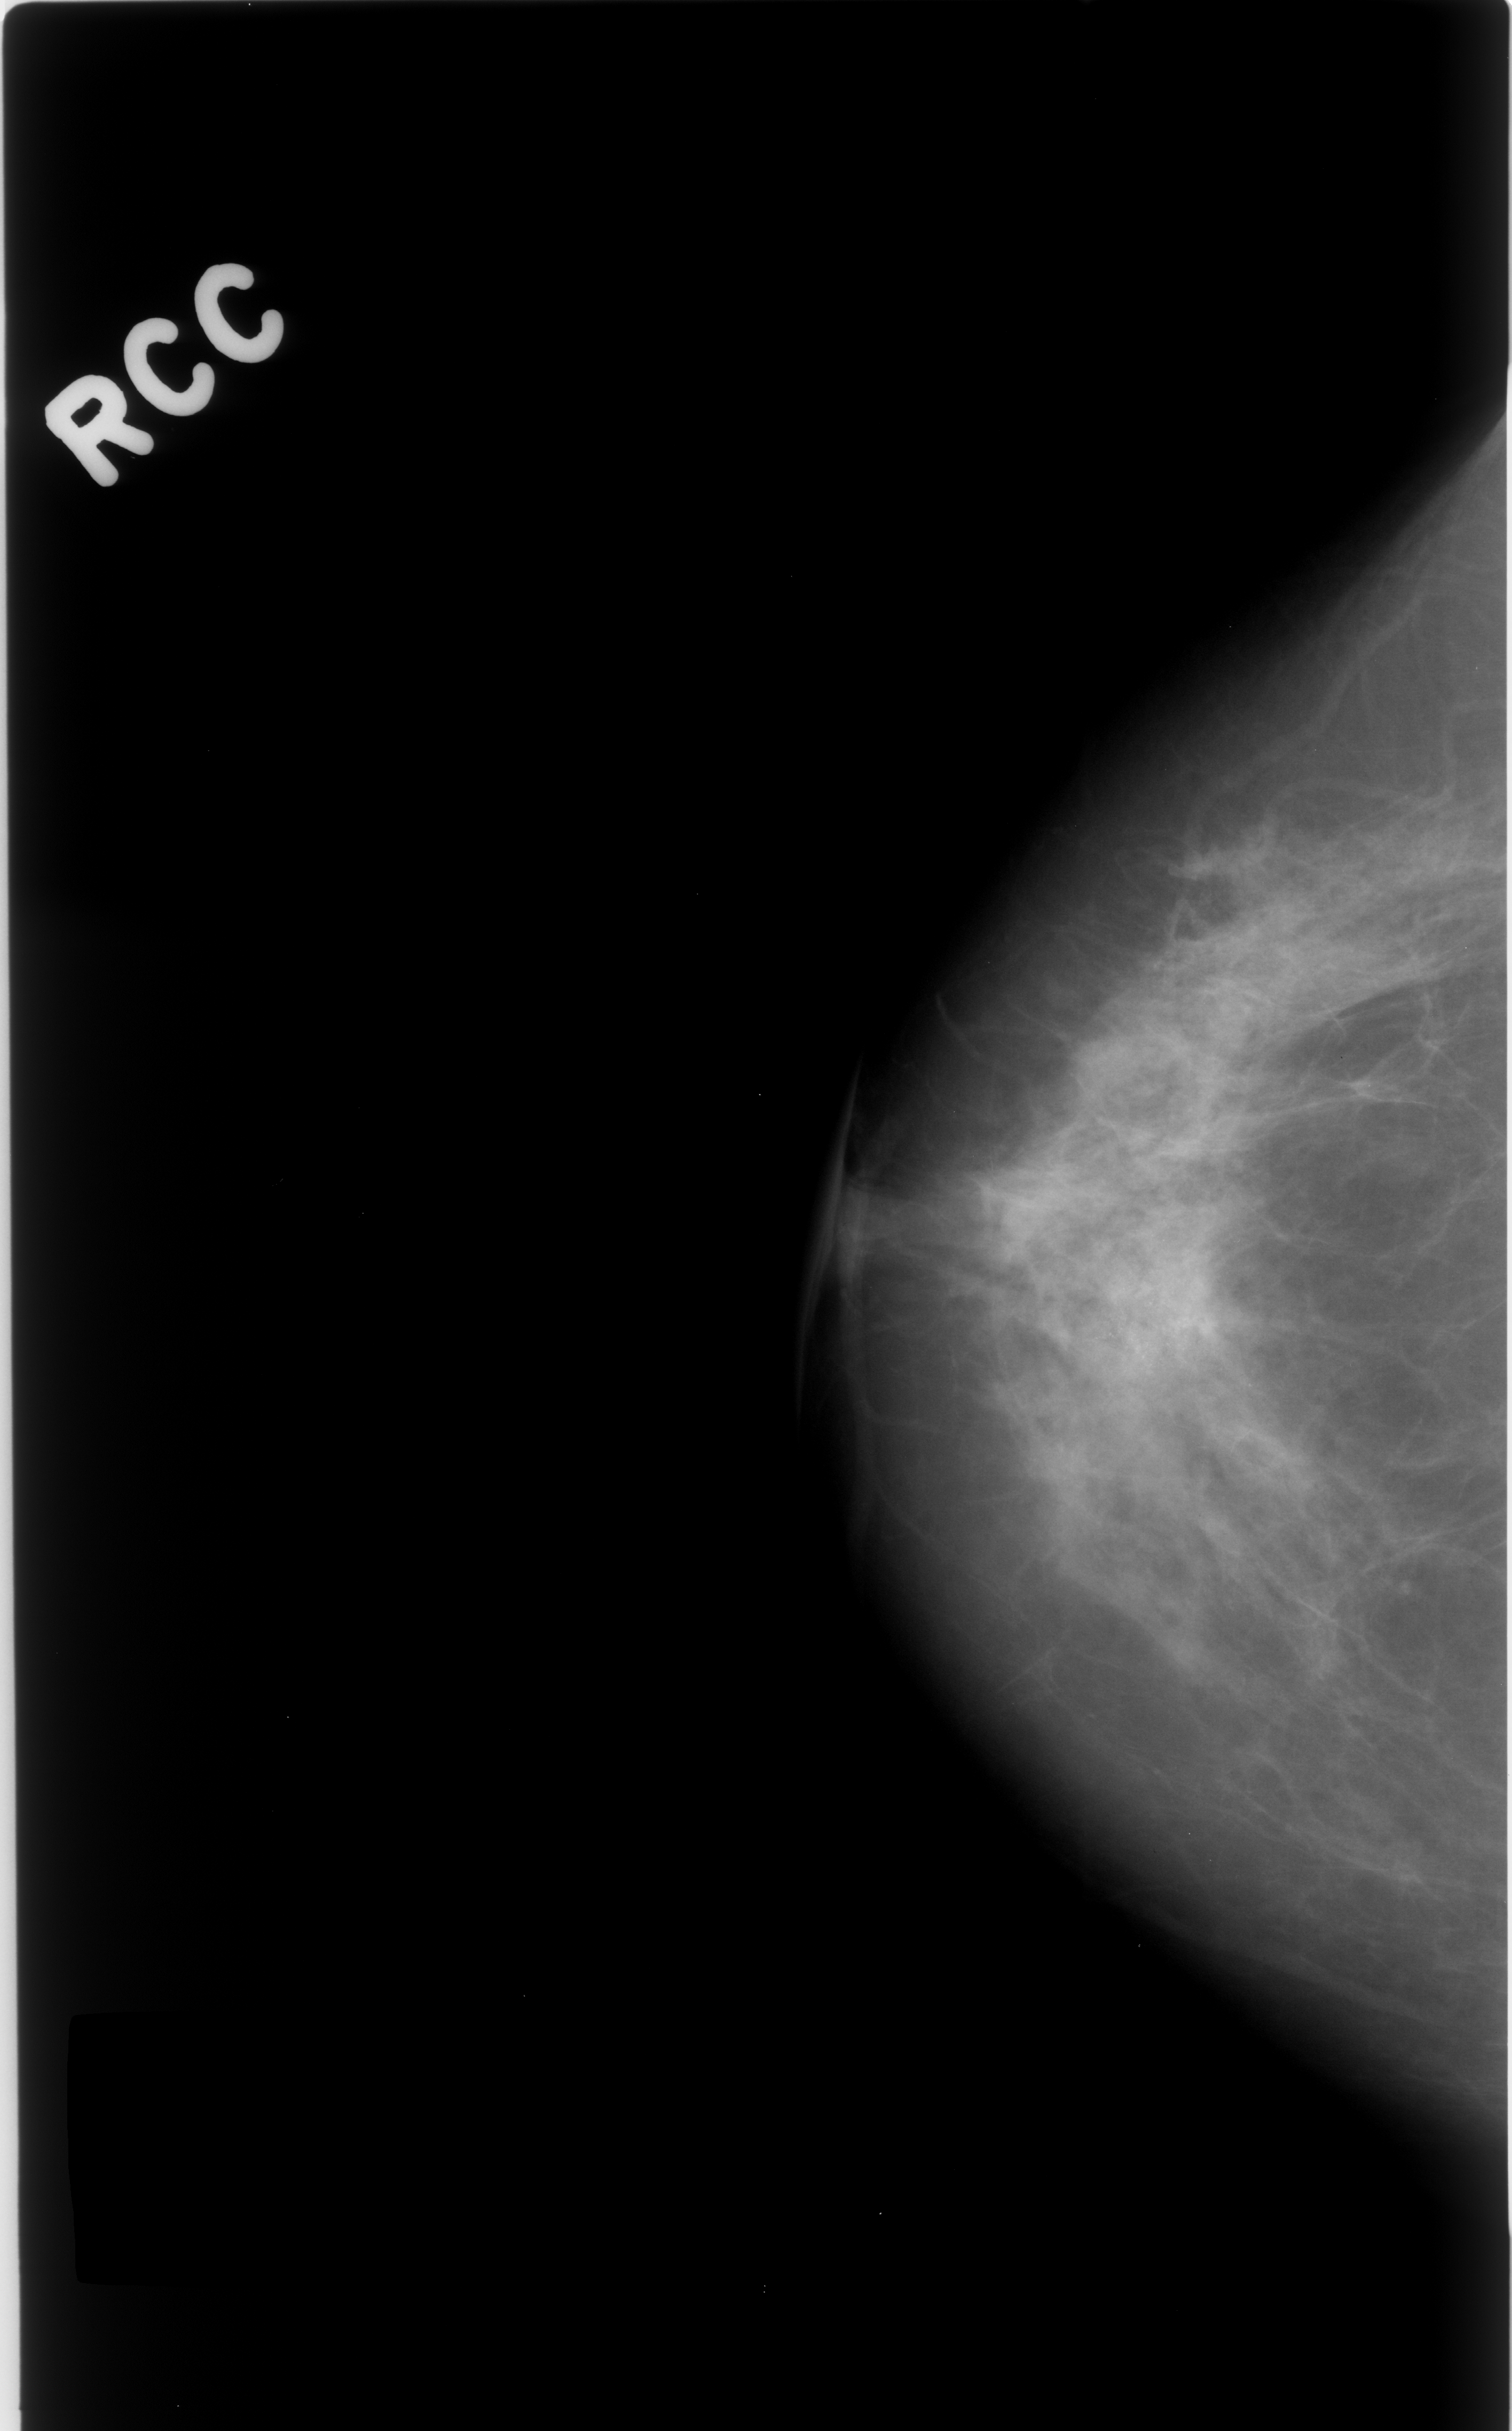
Scanned film-screen mammogram; right breast; CC view; BI-RADS breast density category 2 (scale 1–4); 1512 × 2431 image matrix.
Expert-marked regions of interest on this image (one box per marked abnormality):
- calcifications, morphology amorphous, distribution clustered; BI-RADS assessment category 4; pathology result (as recorded, not read from the image): benign: bounding box [x1, y1, x2, y2] px = [1033, 1174, 1287, 1428]